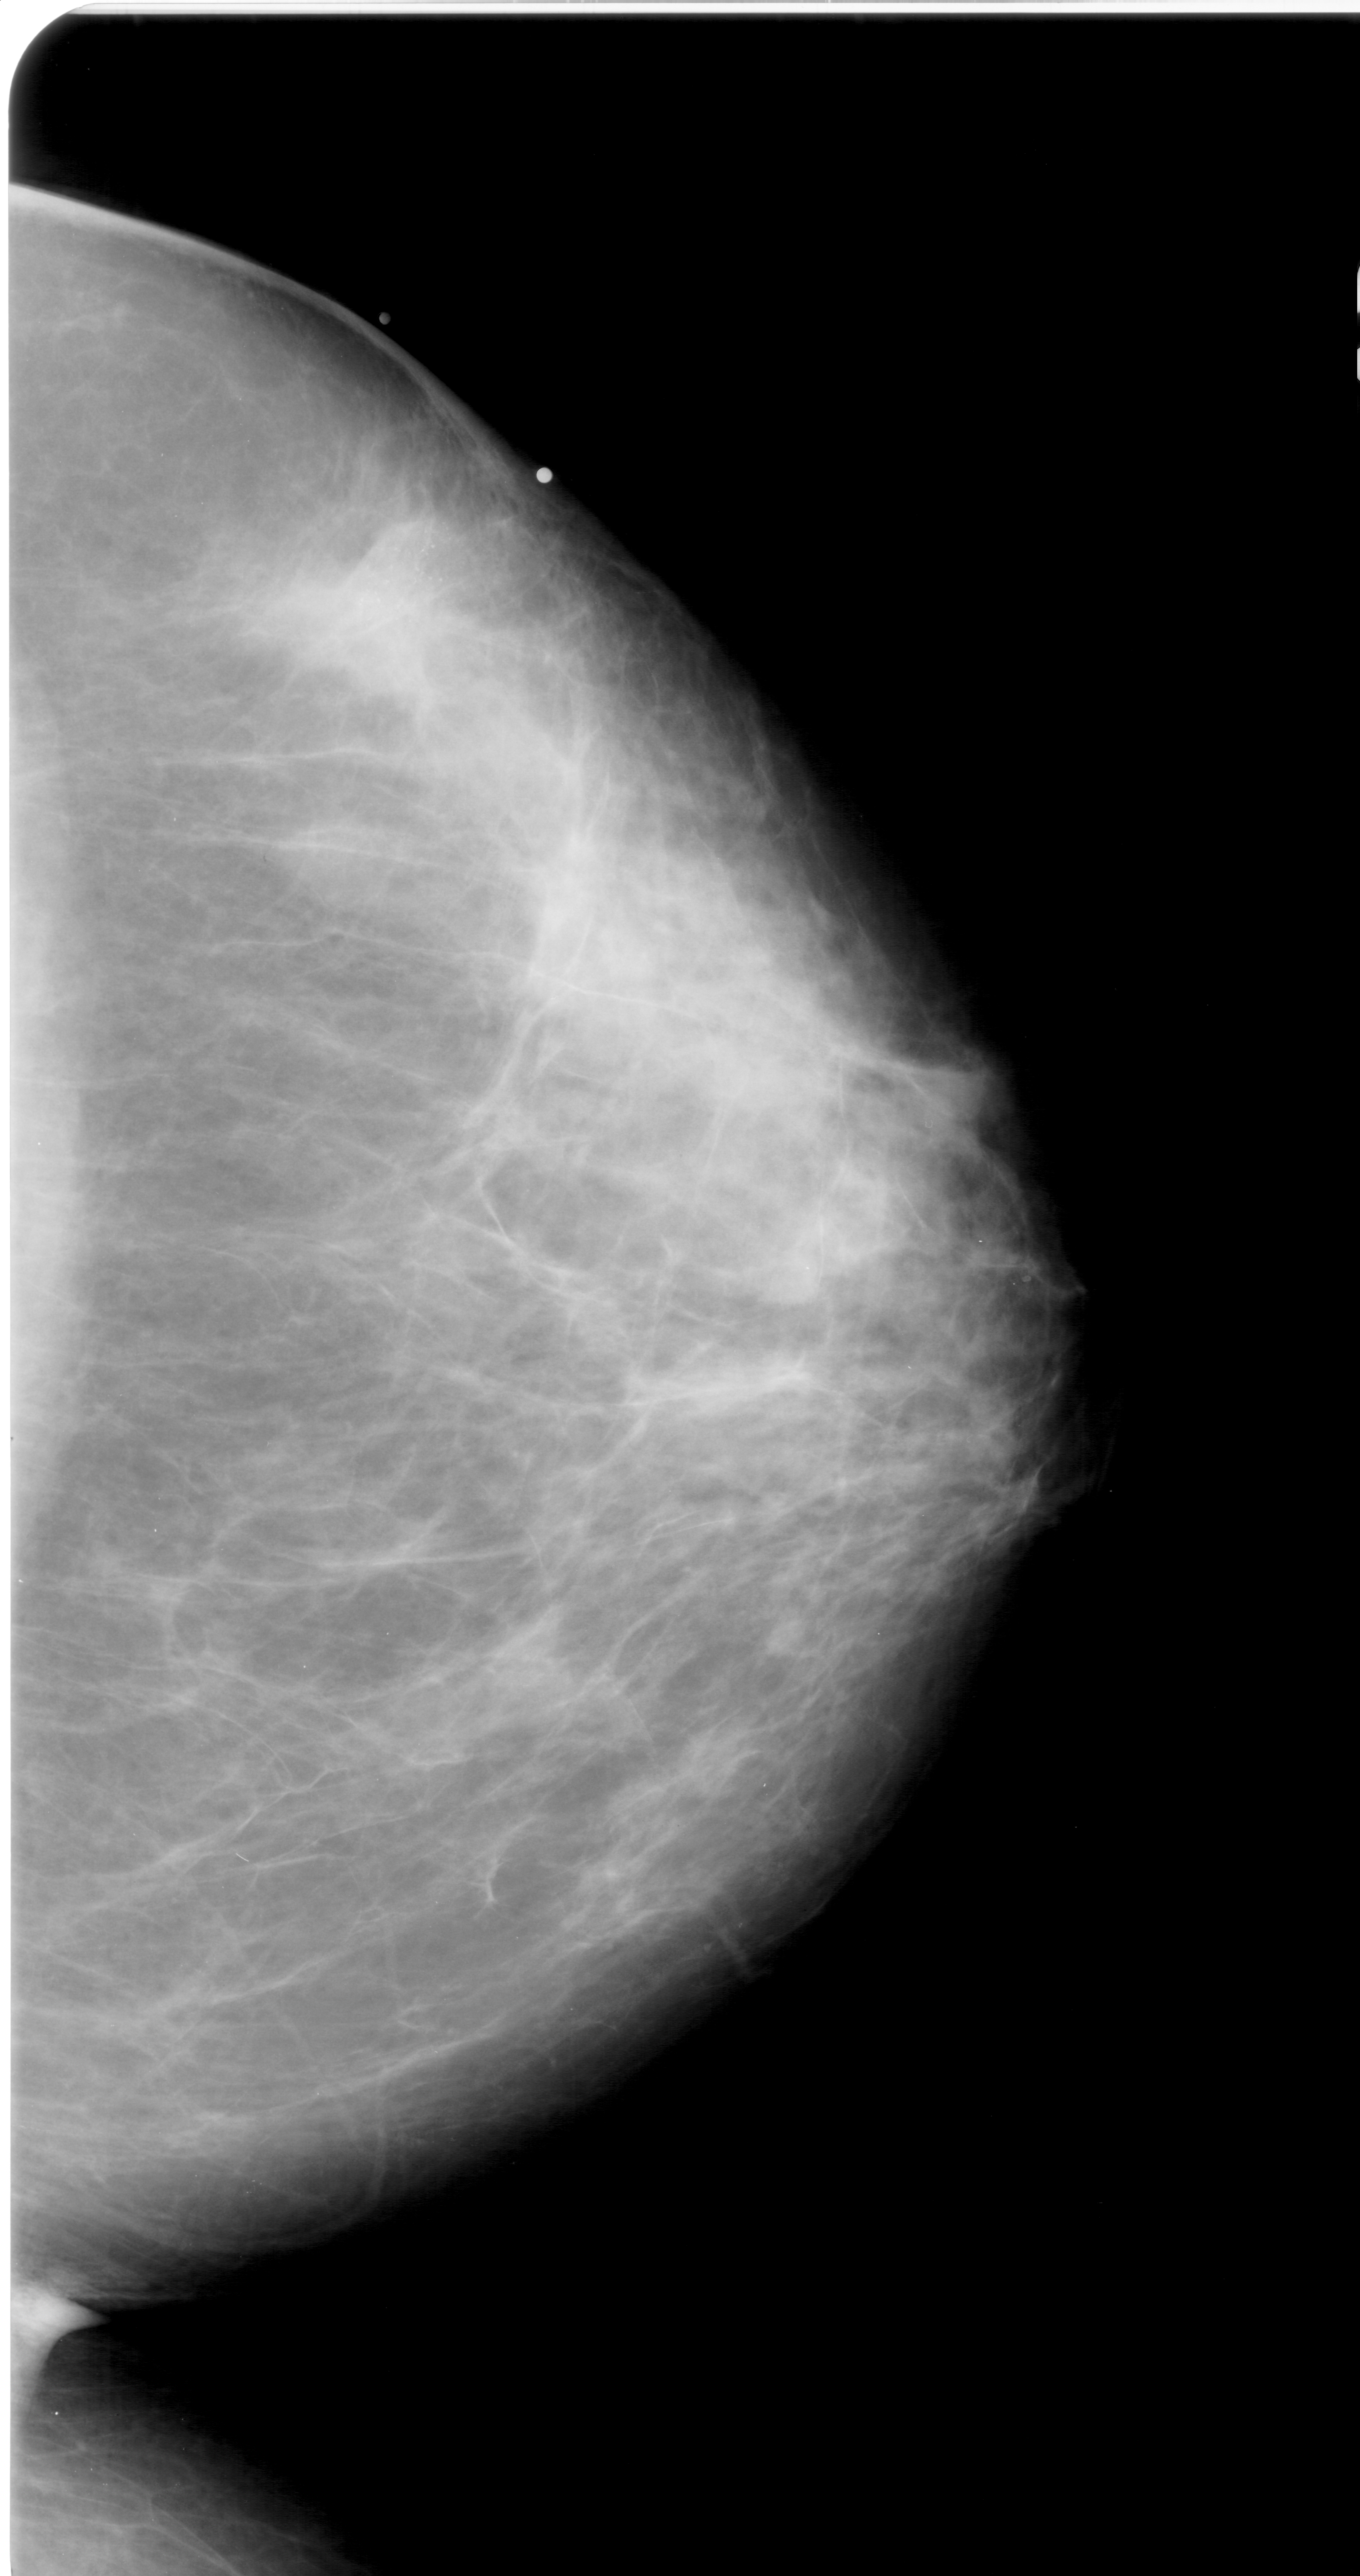
Scanned film-screen mammogram; right breast; CC view.
Radiologist-marked abnormalities on this image: mass, shape irregular, margins spiculated; BI-RADS assessment category 5; pathology (as recorded): malignant.